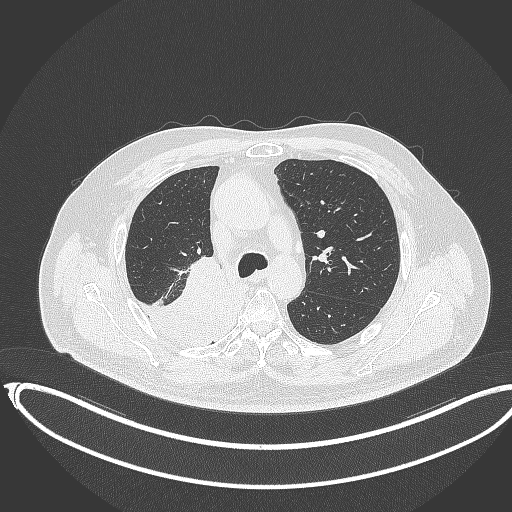
Chest CT, one axial slice. Position 245 of 403 along the scan axis. Lung window (W 1500 / L -600 HU). 1 mm slice thickness. 512 × 512 image matrix, field of view 436 × 436 mm. Male patient, age 68 years. Case-level facts recorded for this patient, not image findings: clinical TNM (as recorded): T2a N0 M0.
Annotated regions visible in this slice (rectangle marked by the reading radiologist):
- lung tumour (recorded histology: adenocarcinoma): bounding box (x1, y1, x2, y2) in pixels: (122, 256, 237, 345)